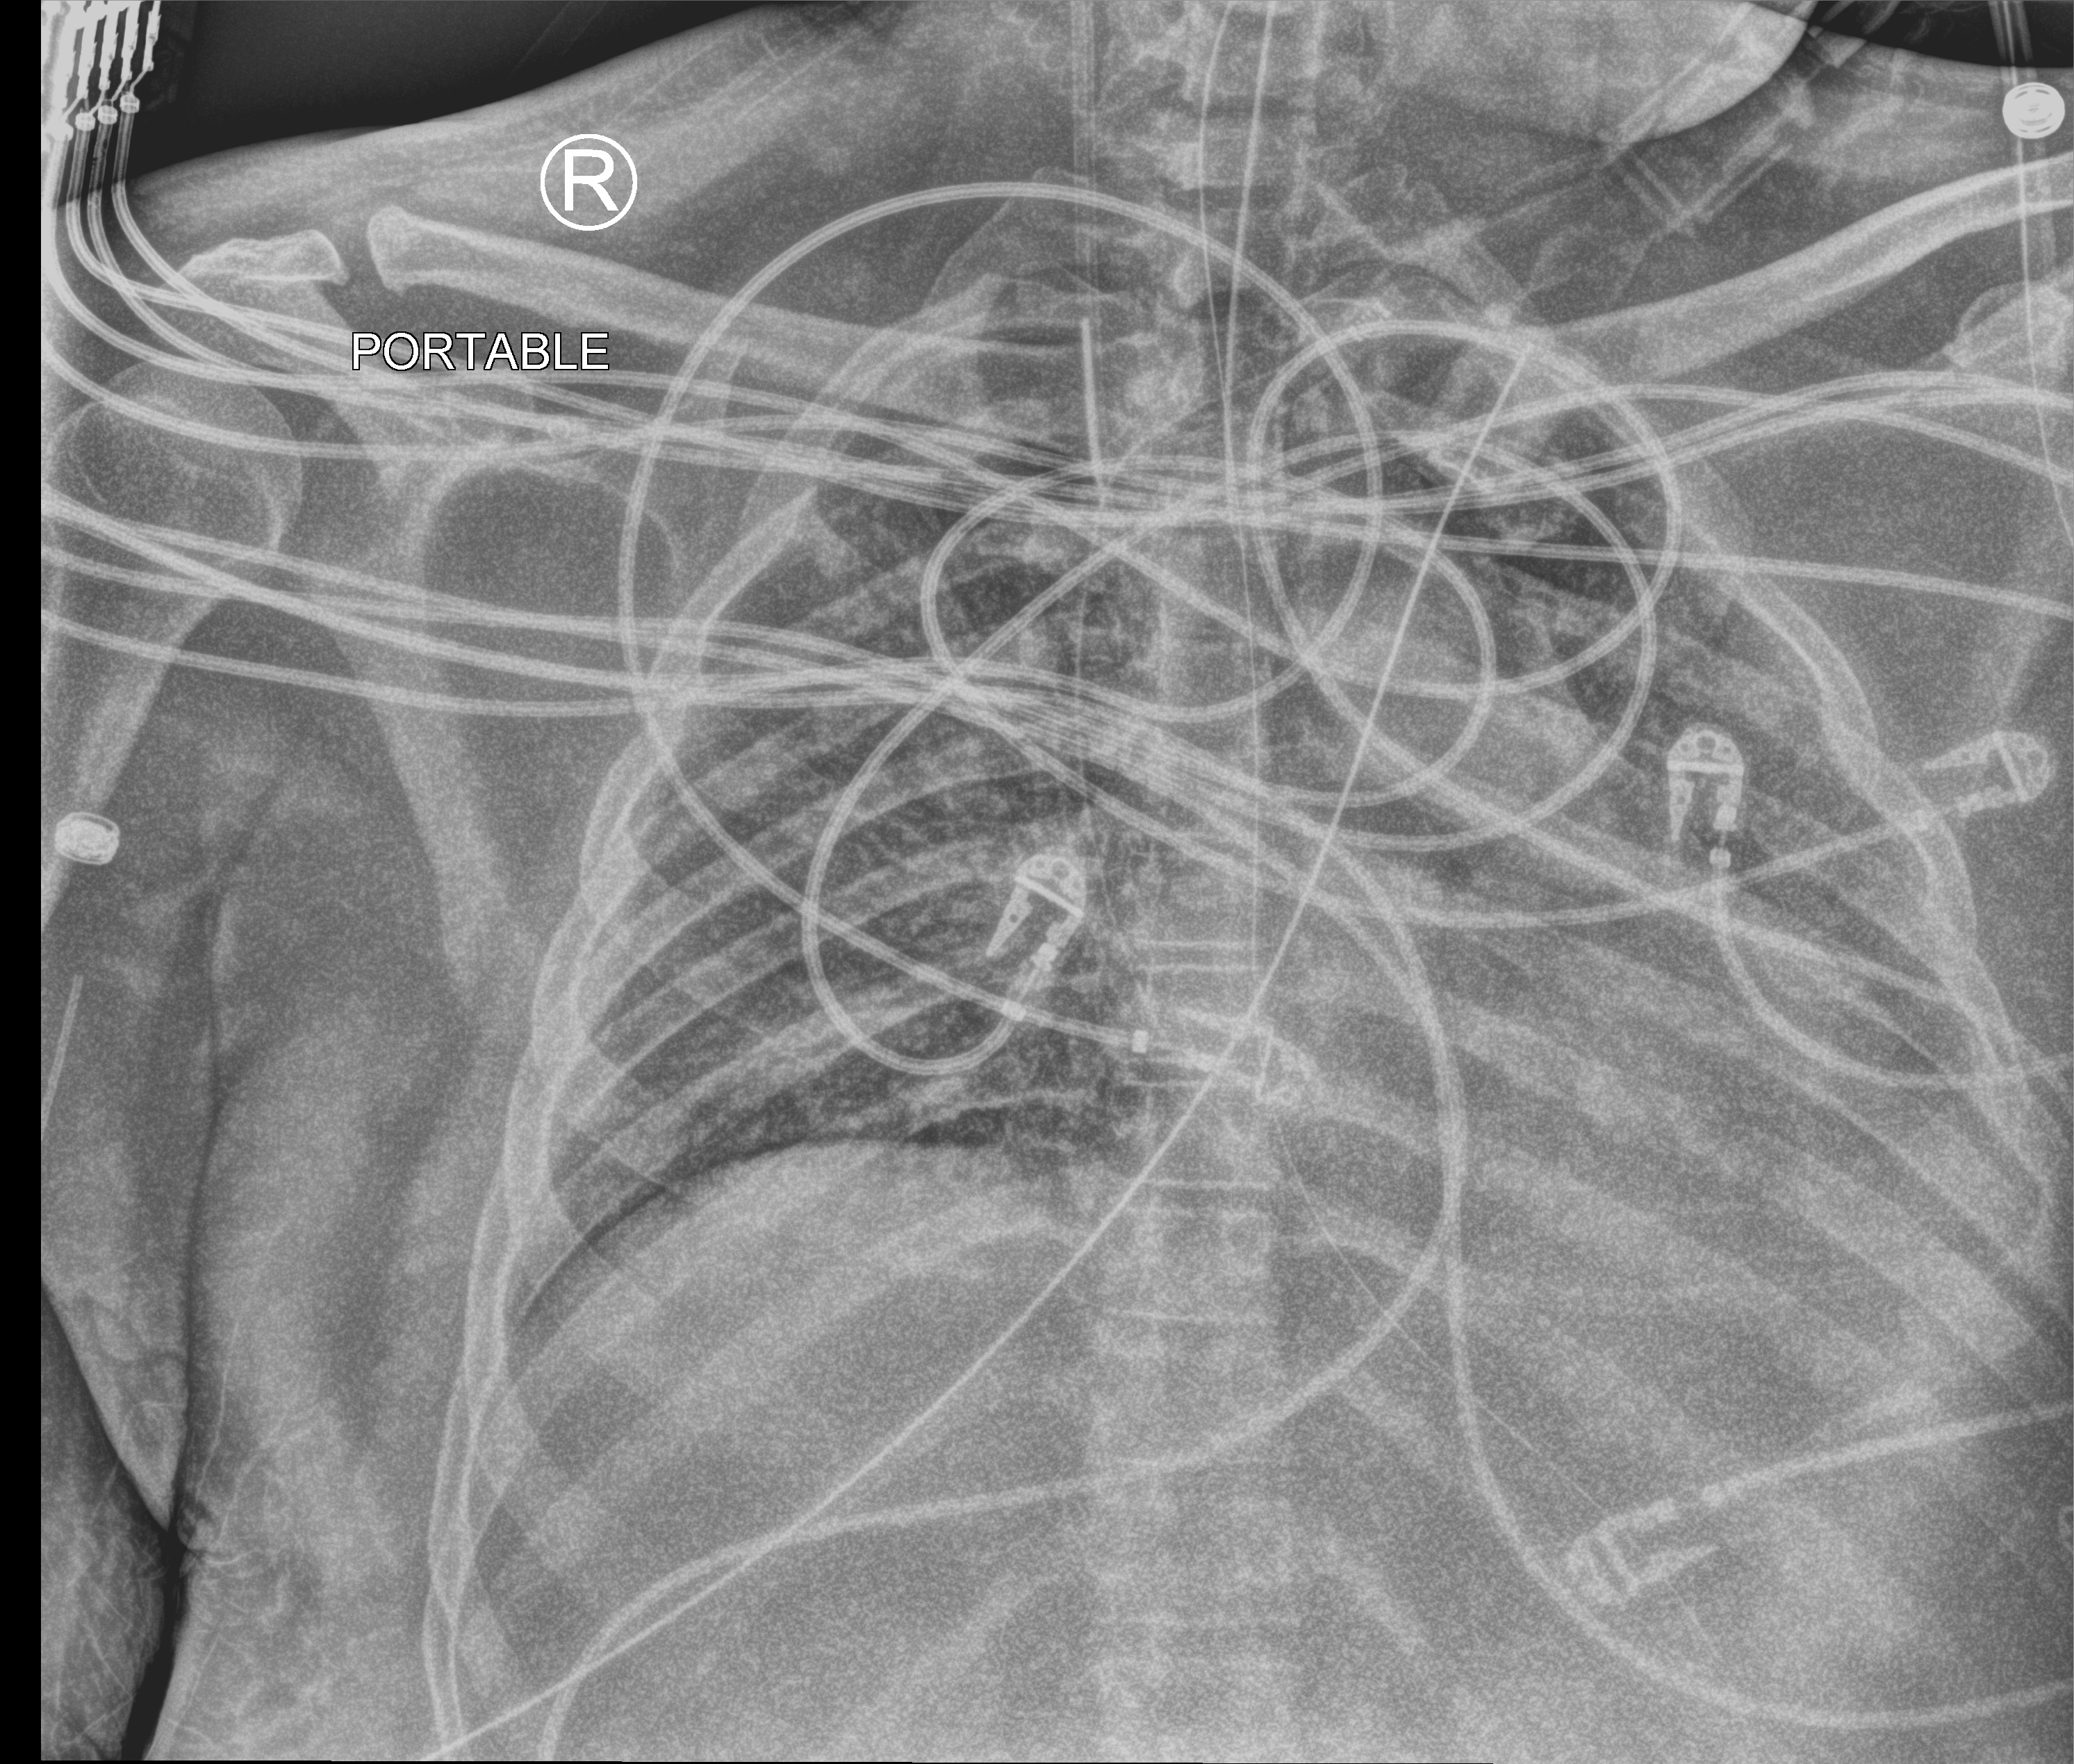
Portable chest radiograph, anteroposterior (AP) projection. Patient hospitalised with COVID-19, aged 18–59 years.
Admission-level facts for this patient (not findings on this image; timing relative to this image not recorded): length of hospital stay: 19 days; admitted to intensive care during this hospital stay: yes; mechanically ventilated during this hospital stay: yes.